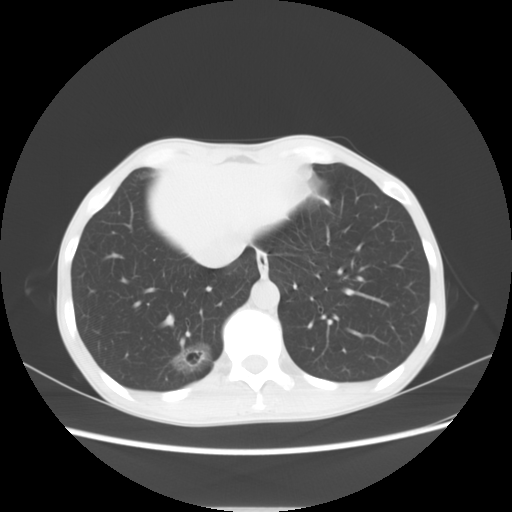
Chest CT, one axial slice; slice 19 of 69 in the series (ordered by position); 120 kVp; lung window (W 1500 / L -600 HU); 5 mm slice thickness; 512 × 512 image matrix. Patient: female, 51 years. Case-level facts recorded for this patient, not image findings: clinical TNM (as recorded): T1c N0 M0.
Outlined on this slice (bounding box drawn by a radiologist):
- lung tumour (recorded histology: adenocarcinoma): box from (x=166, y=336) to (x=218, y=378) px